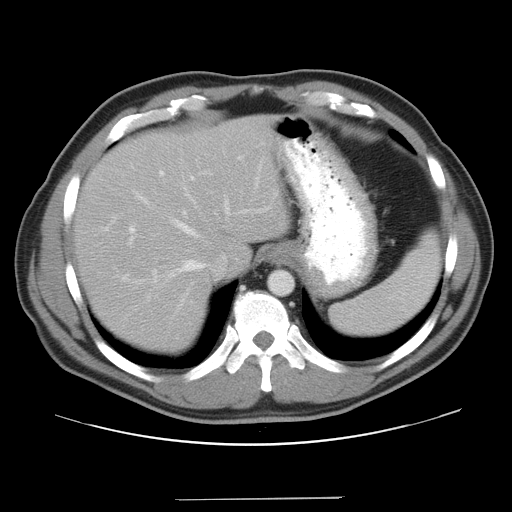
Contrast-enhanced abdominal CT, one axial slice. 120 kVp. Intravenous contrast given. Soft-tissue window (W 400 / L 40 HU). 7.5 mm slice thickness. 512 × 512 image matrix. Male patient, age 46 years. From the clinical record (not read from this slice): diagnosis: colorectal cancer liver metastases, imaged before liver resection; multiple liver metastases: yes; largest metastasis: 1 cm.
Structures marked on this image (manually delineated by an expert):
- hepatic veins: bounding box (x1, y1, x2, y2) in pixels: (133, 157, 271, 284)
- liver: (77, 119, 283, 349)
- planned liver remnant (the part of the liver to remain after resection): (77, 119, 283, 349)
- portal vein (with intrahepatic branches): (129, 156, 244, 244)